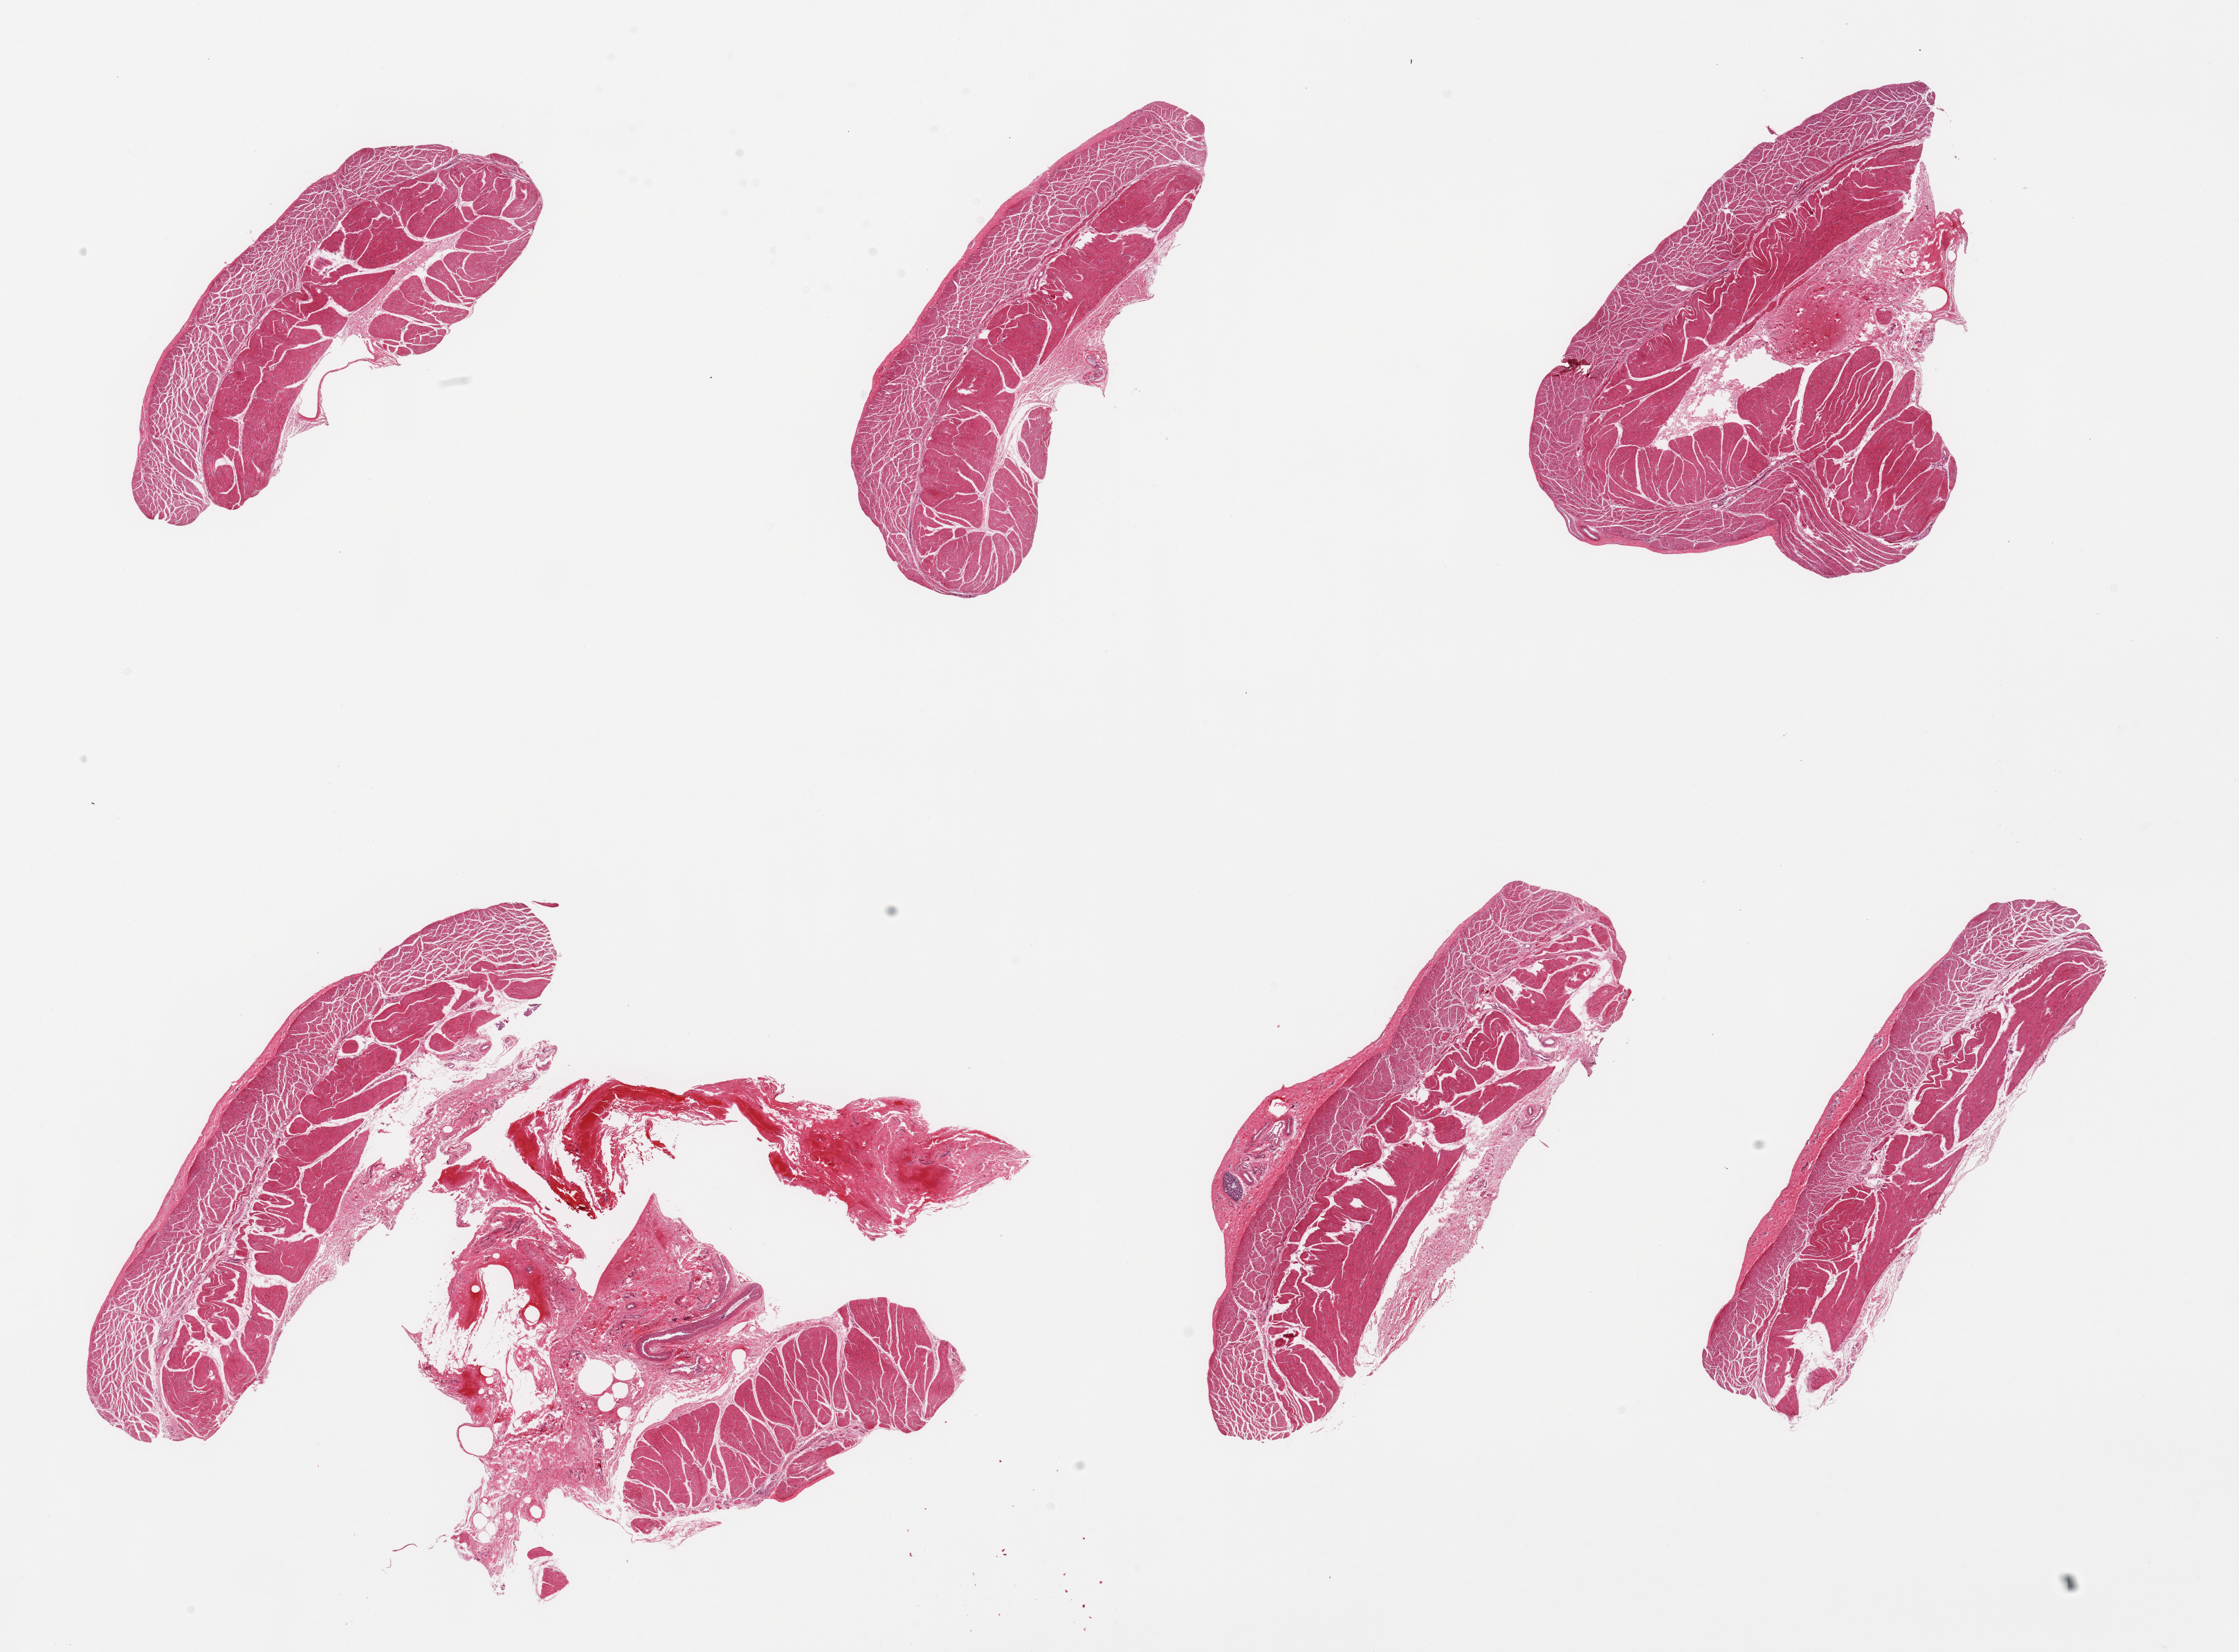
Whole-slide image, H&E stain, low-resolution overview of the scanned area, about 25.6 x 18.9 mm; PAXgene-fixed paraffin-embedded (PFPE) section; section of esophageal muscle (target tissue); tissue donor sample. Donor: female.
Pathologist's review note for this sample: 7 pieces; includes some attached submucosal glands and larger vessels.